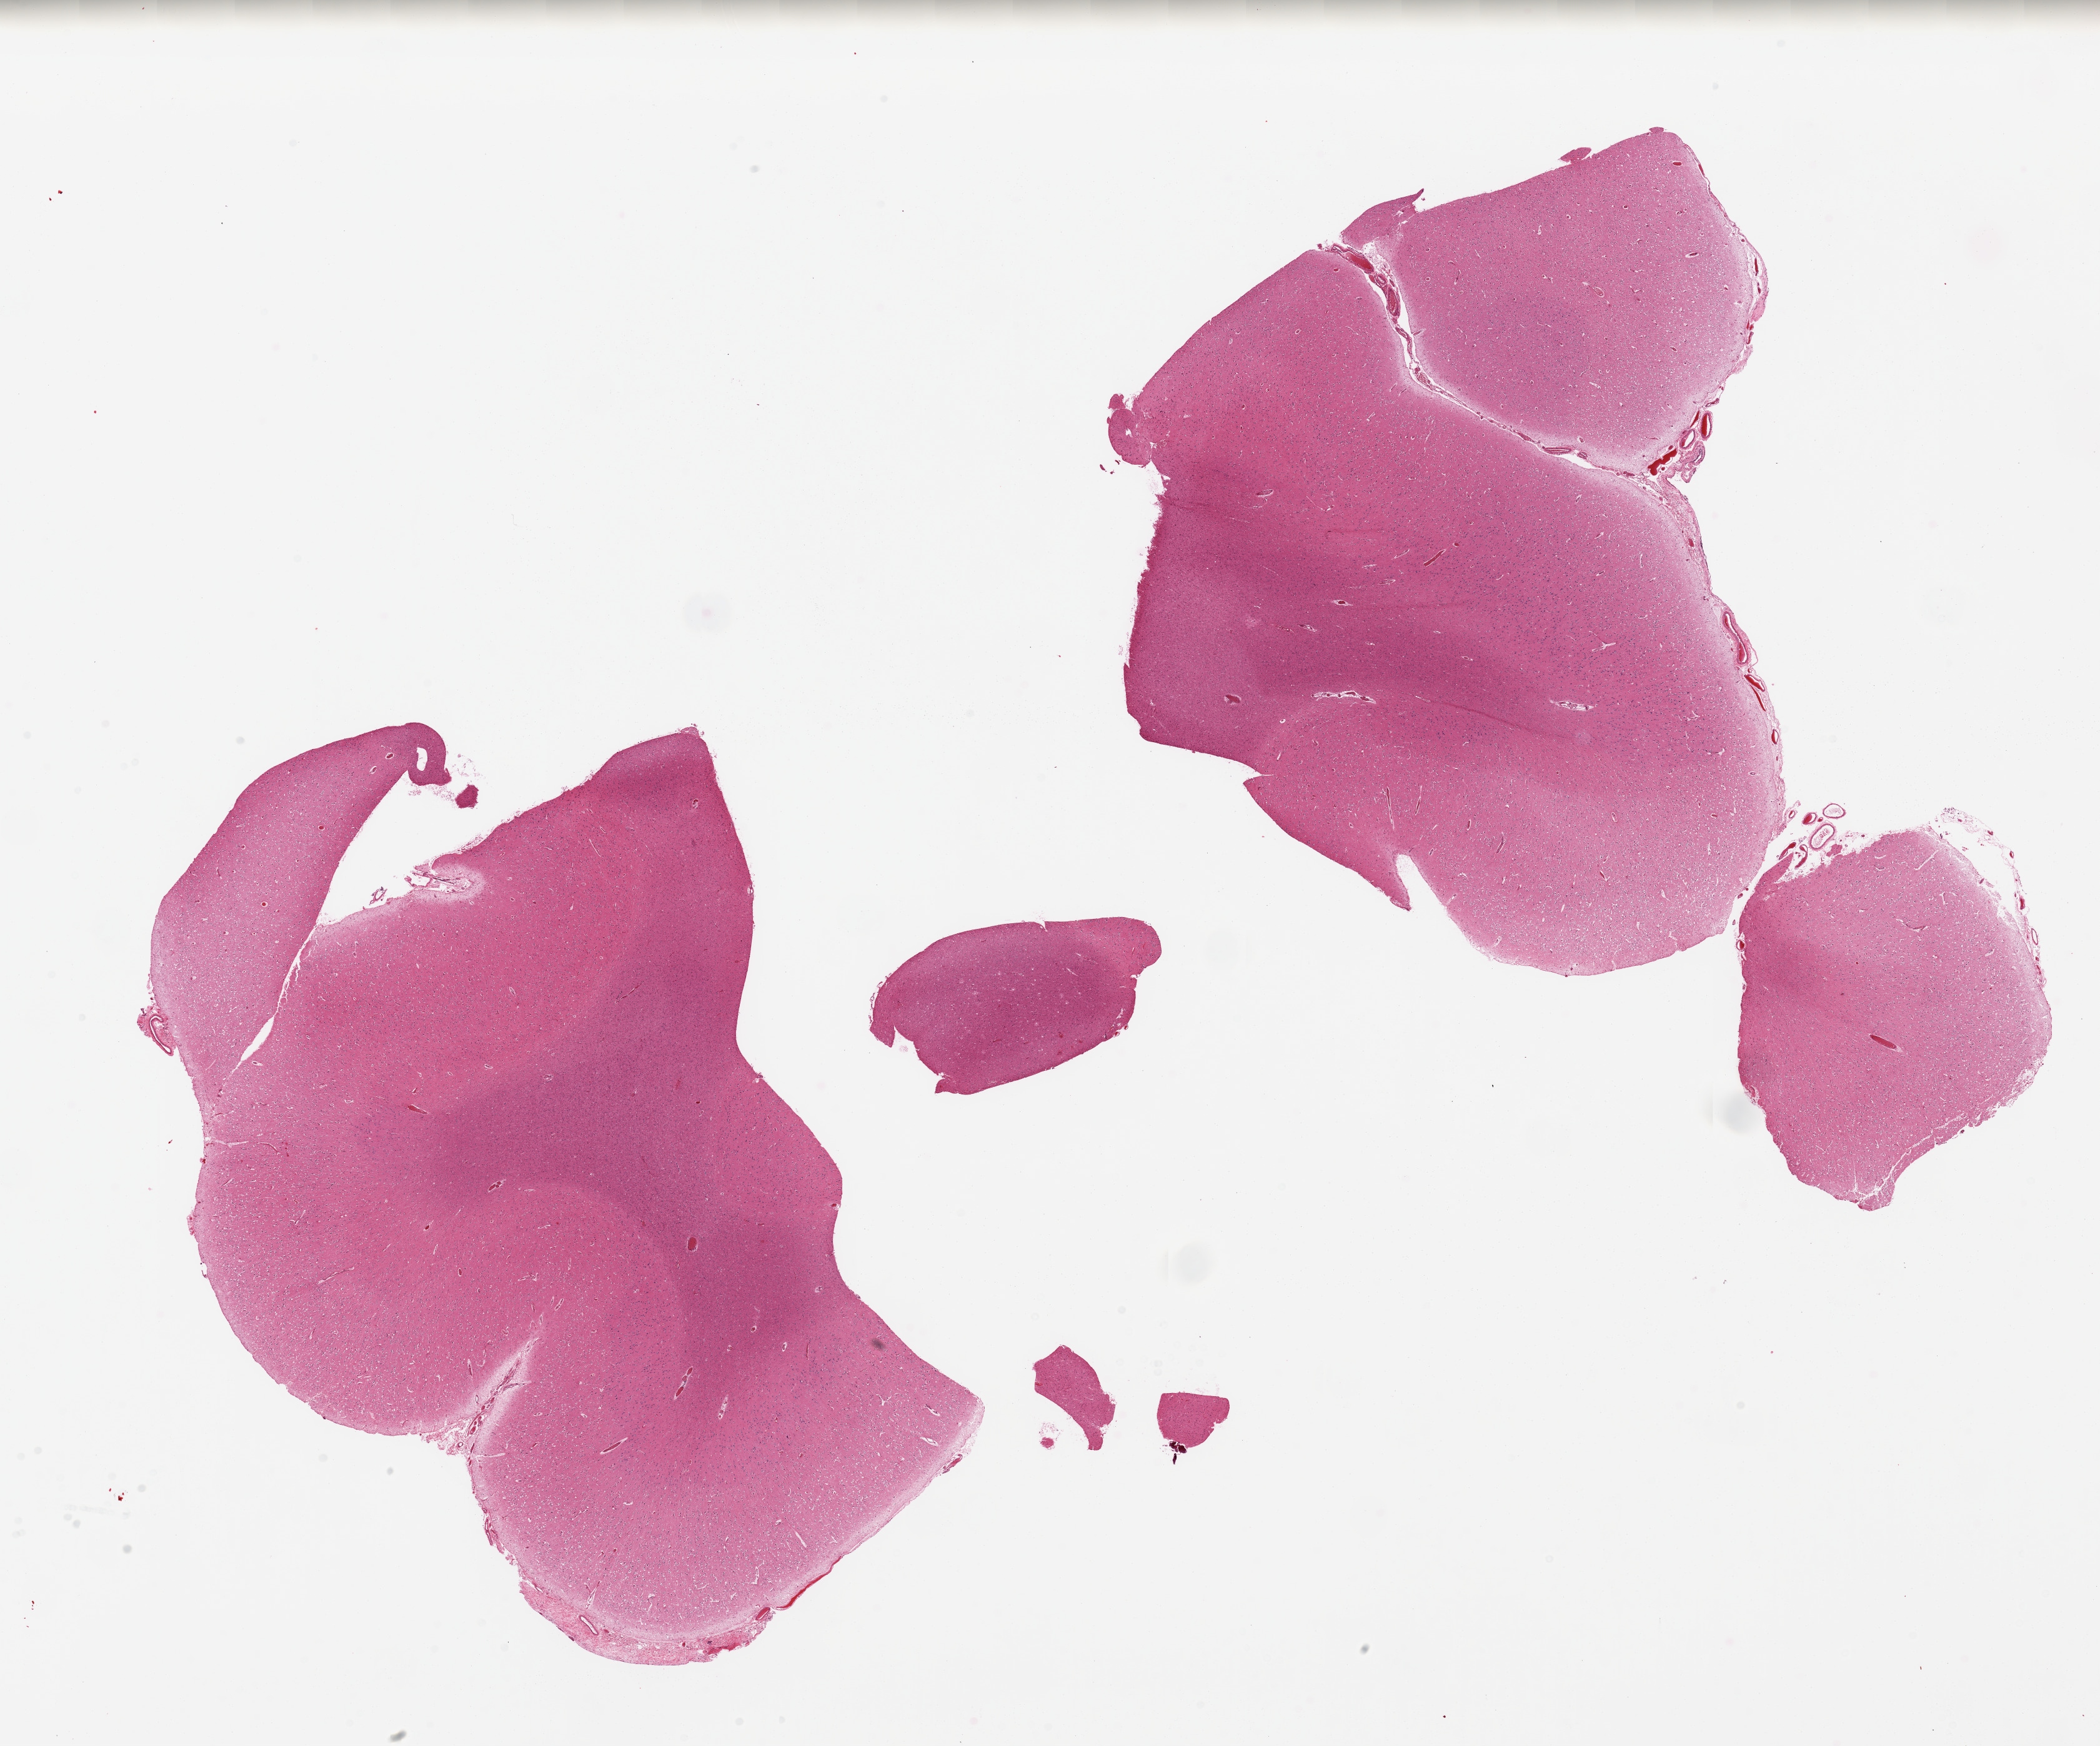
Digitized H&E-stained section, whole scanned area (about 26.6 x 22.1 mm) shown as a low-resolution overview, PAXgene-fixed, paraffin-embedded tissue, target tissue: cerebral cortex, tissue donor sample.
Pathologist's review note for this sample: 2 pieces, no abnormalities.